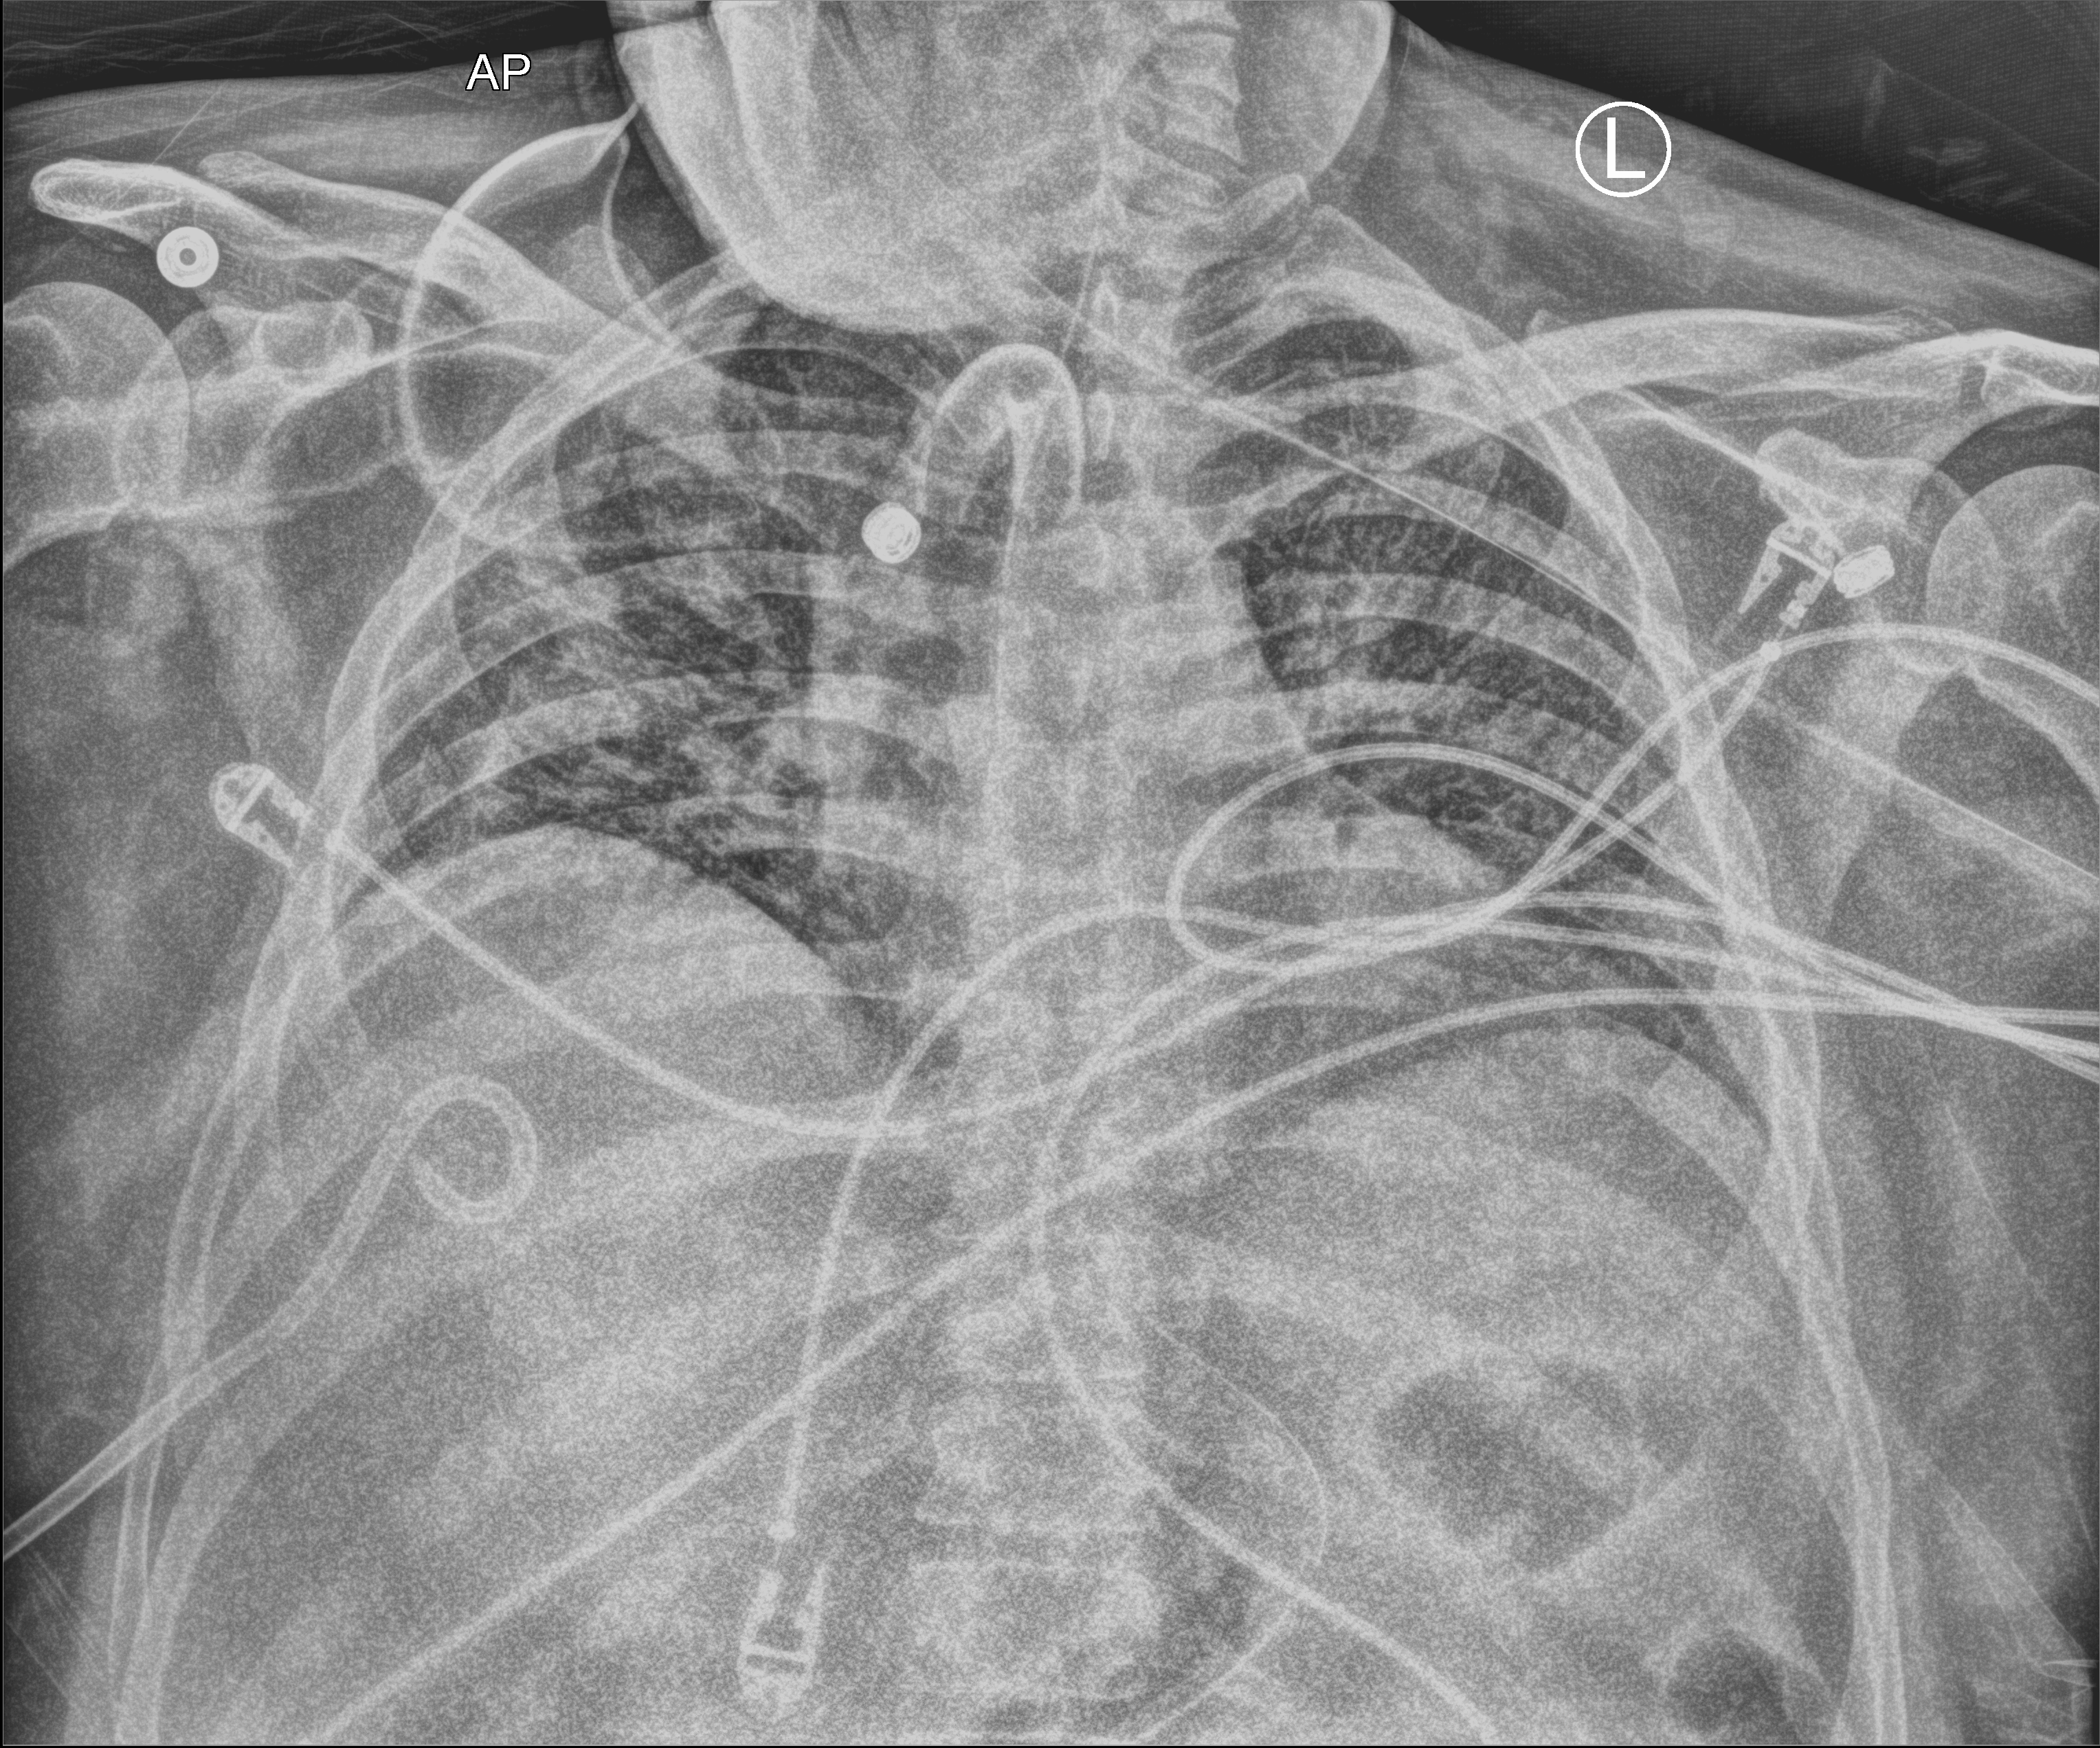
Chest X-ray (portable); anteroposterior (AP) projection. Male patient hospitalised with COVID-19, age 18–59 years.
From the hospital-stay record, not from the radiograph (when in the stay this image was taken is not recorded):
- COPD (admission record): no
- mechanically ventilated during this hospital stay: yes